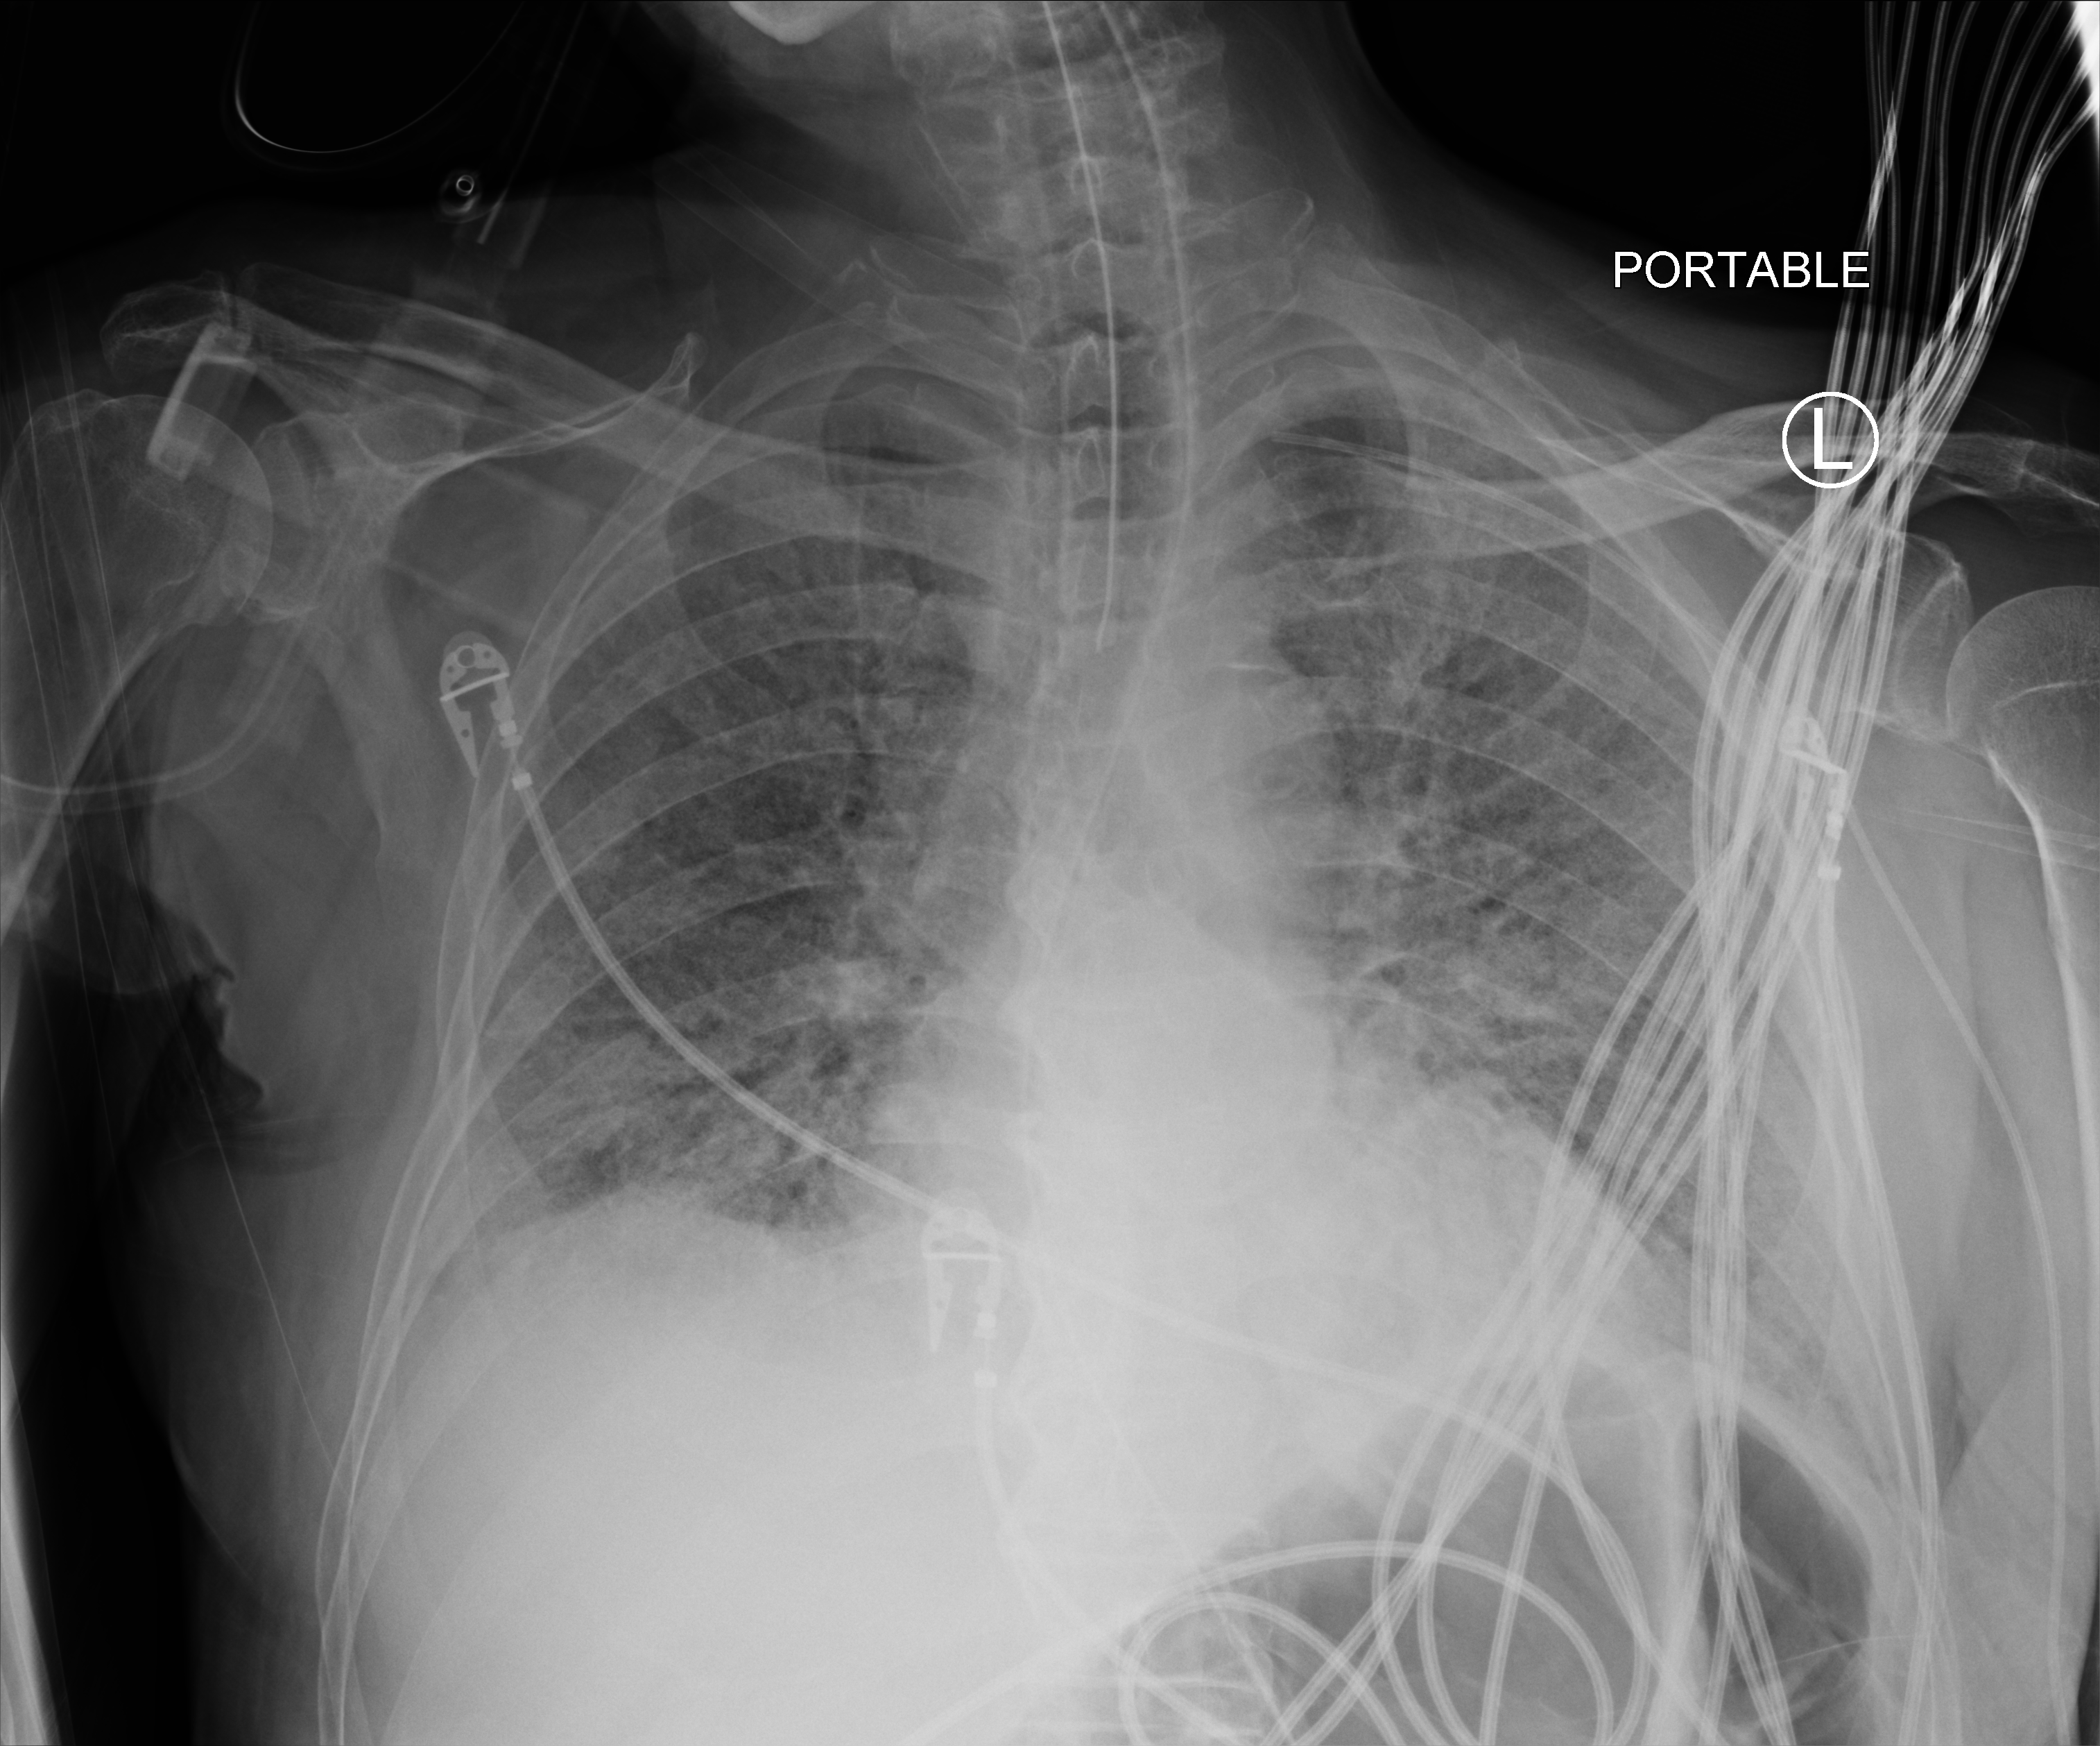
Chest X-ray (portable); anteroposterior (AP) projection. Male patient hospitalised with COVID-19, age 75–90 years.
From the hospital-stay record, not from the radiograph (when in the stay this image was taken is not recorded): length of hospital stay: 30 days; admitted to intensive care during this hospital stay: yes; mechanically ventilated during this hospital stay: yes.